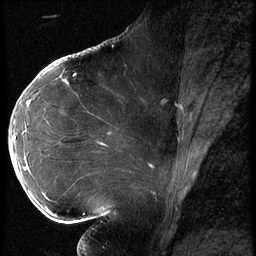
Breast MRI (dynamic contrast-enhanced), one sagittal slice. Position 33 of 62 along the scan axis. 3 images stored at this slice position (order not interpretable as contrast timing). 1.5 T. TE 4.2 ms, TR 9 ms. 2.5 mm slice thickness. 256 × 256 image matrix, field of view 180 × 180 mm. Patient: female, 43 years. From the clinical record (not read from this slice): setting: breast cancer imaged before/during neoadjuvant chemotherapy; receptor status: HER2-positive.
Annotated regions visible in this slice (semi-automatically segmented with operator editing):
- analysis volume of interest (the breast-tissue region the enhancement analysis was run in; not a lesion): bounding box [x1, y1, x2, y2] px = [10, 90, 82, 203]
- tumour enhancement mask (voxels above the 140 % enhancement threshold inside the analysis volume of interest): [11, 101, 30, 165]